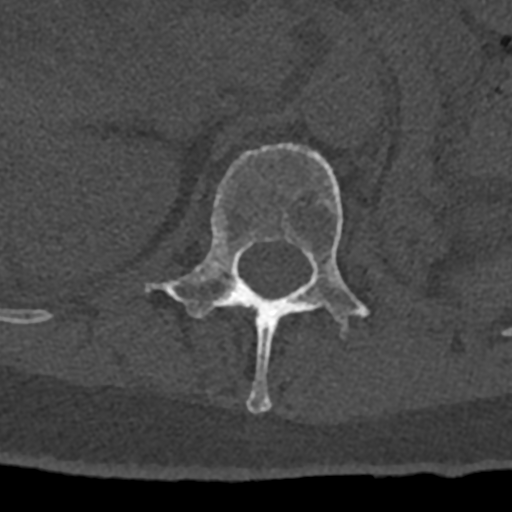
CT including the spine, one axial slice; position 440 of 797 along the scan axis; reconstruction kernel Br40s/3; 120 kVp; bone window (W 1800 / L 400 HU); 512 × 512 image matrix, field of view 160 × 160 mm. Male patient, age 74 years. Case-level facts recorded for this patient, not image findings: primary cancer: renal; vertebrae with lytic lesions (as recorded): T10, L1, L2, L3, L4, L5.
Annotated regions visible in this slice (semi-automatically segmented with operator editing):
- L1 vertebra: bounding box [x1, y1, x2, y2] px = [145, 143, 371, 413]
- T12 vertebra: [228, 304, 235, 307]